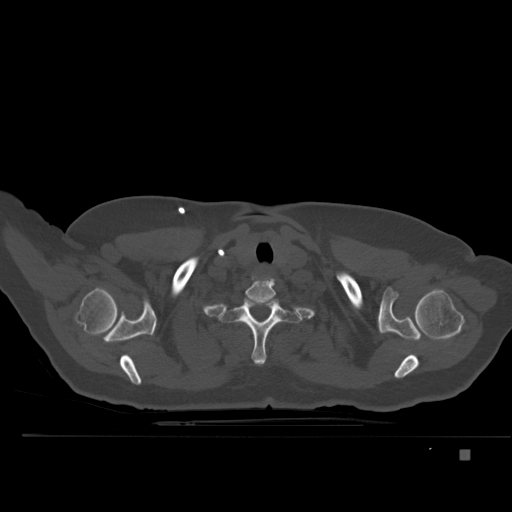
CT including the spine, one axial slice; position 404 of 477 along the scan axis; bone window (W 1800 / L 400 HU); 512 × 512 image matrix, field of view 422 × 422 mm. Patient: female, 74 years. From the clinical record (not read from this slice): primary cancer: colon.
Structures marked on this image (semi-automatically segmented with operator editing):
- T1 vertebra: bounding box [x1, y1, x2, y2] px = [234, 296, 286, 365]
- T2 vertebra: [276, 323, 279, 325]